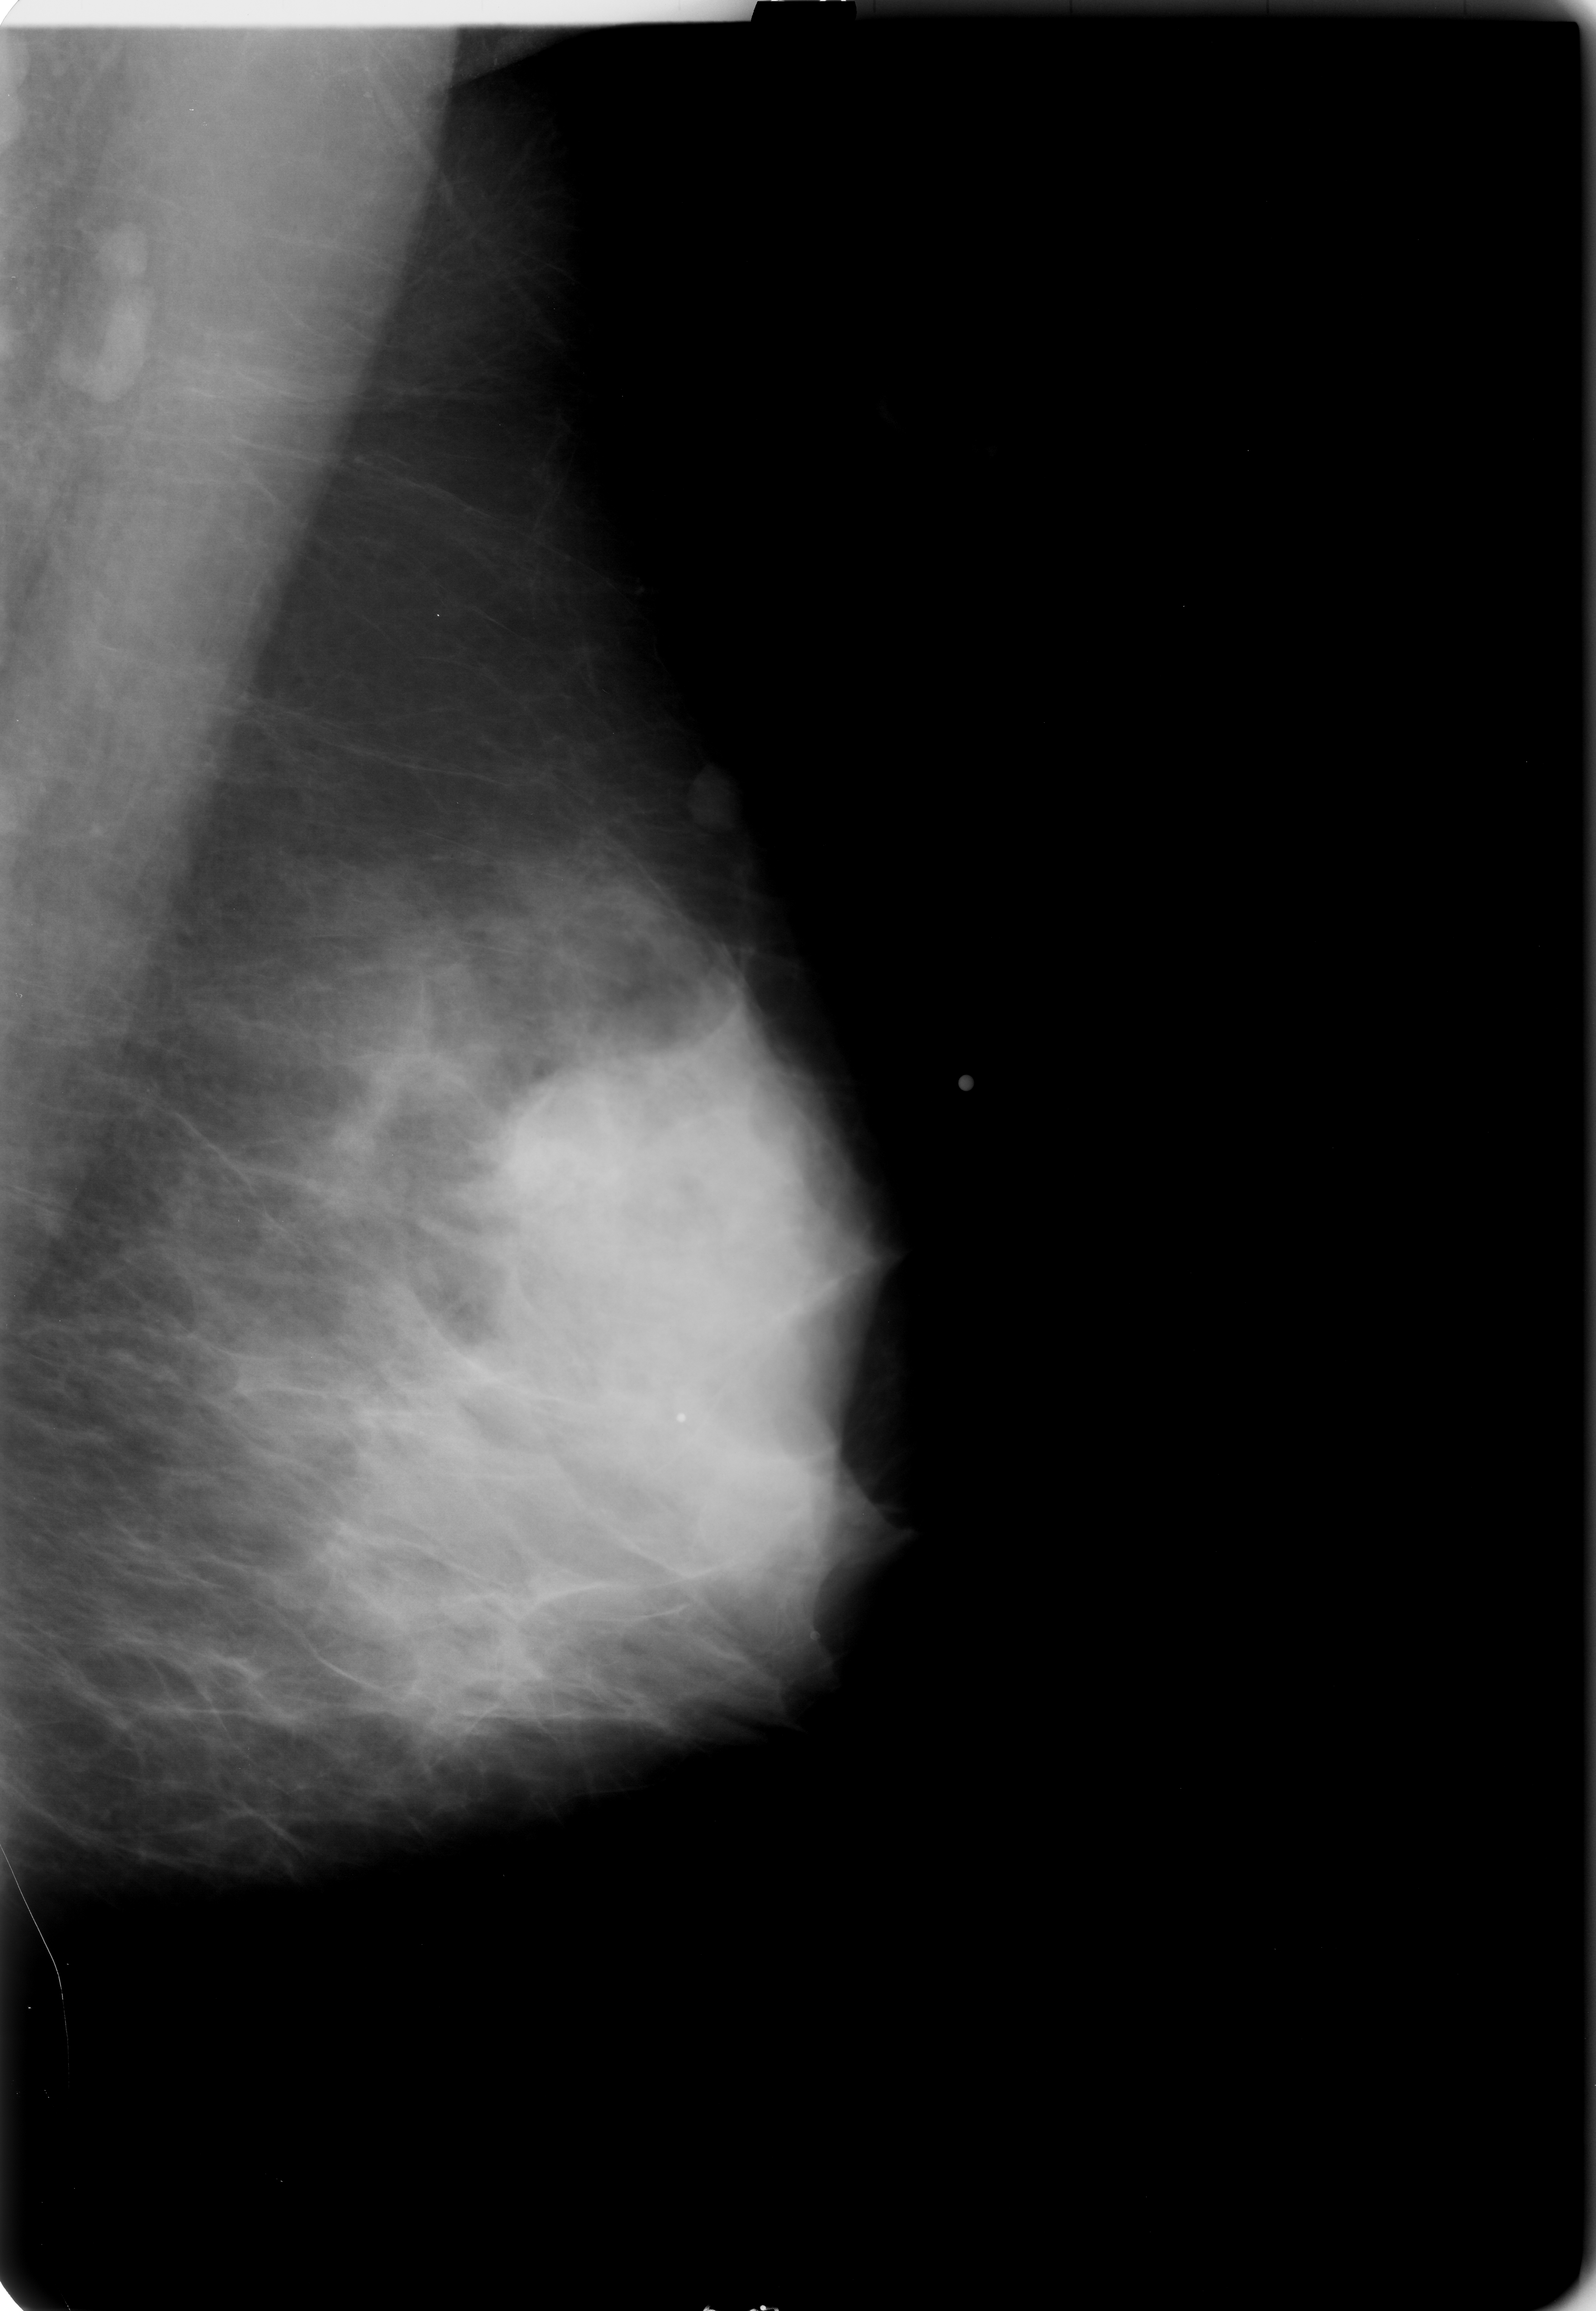
Digitized screen-film mammogram; left breast; MLO view; breast composition: extremely dense (BI-RADS density category 4 of 4).
Marked abnormality: mass, shape focal asymmetric density; BI-RADS assessment category 3; subtlety rating 1 on a 1 (subtle) to 5 (obvious) scale; pathology (as recorded): malignant.